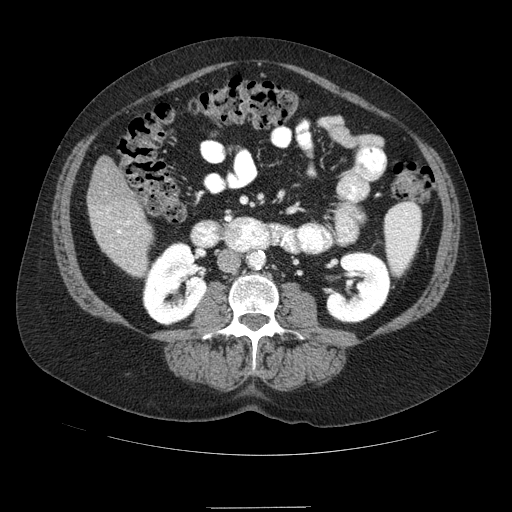
Contrast-enhanced abdominal CT (liver protocol), one axial slice; position 21 of 89 along the scan axis; reconstruction kernel STANDARD; soft-tissue window (W 400 / L 40 HU); 2.5 mm slice thickness; 512 × 512 image matrix, field of view 400 × 400 mm. From the clinical record (not read from this slice): diagnosis: hepatocellular carcinoma (patient treated with transarterial chemoembolisation; whether this scan precedes or follows treatment is not stated here); TNM stage (as recorded): Stage-IIIB; Child-Pugh class: A; tumour nodularity: multinodular.
Structures marked on this image (semi-automatic segmentation, software-assisted and operator-edited):
- liver parenchyma outside the tumour (the mass and vessels are separate outlines, so this box may not span the whole liver): bounding box [x1, y1, x2, y2] px = [88, 156, 152, 274]
- liver vessels: [117, 222, 129, 233]